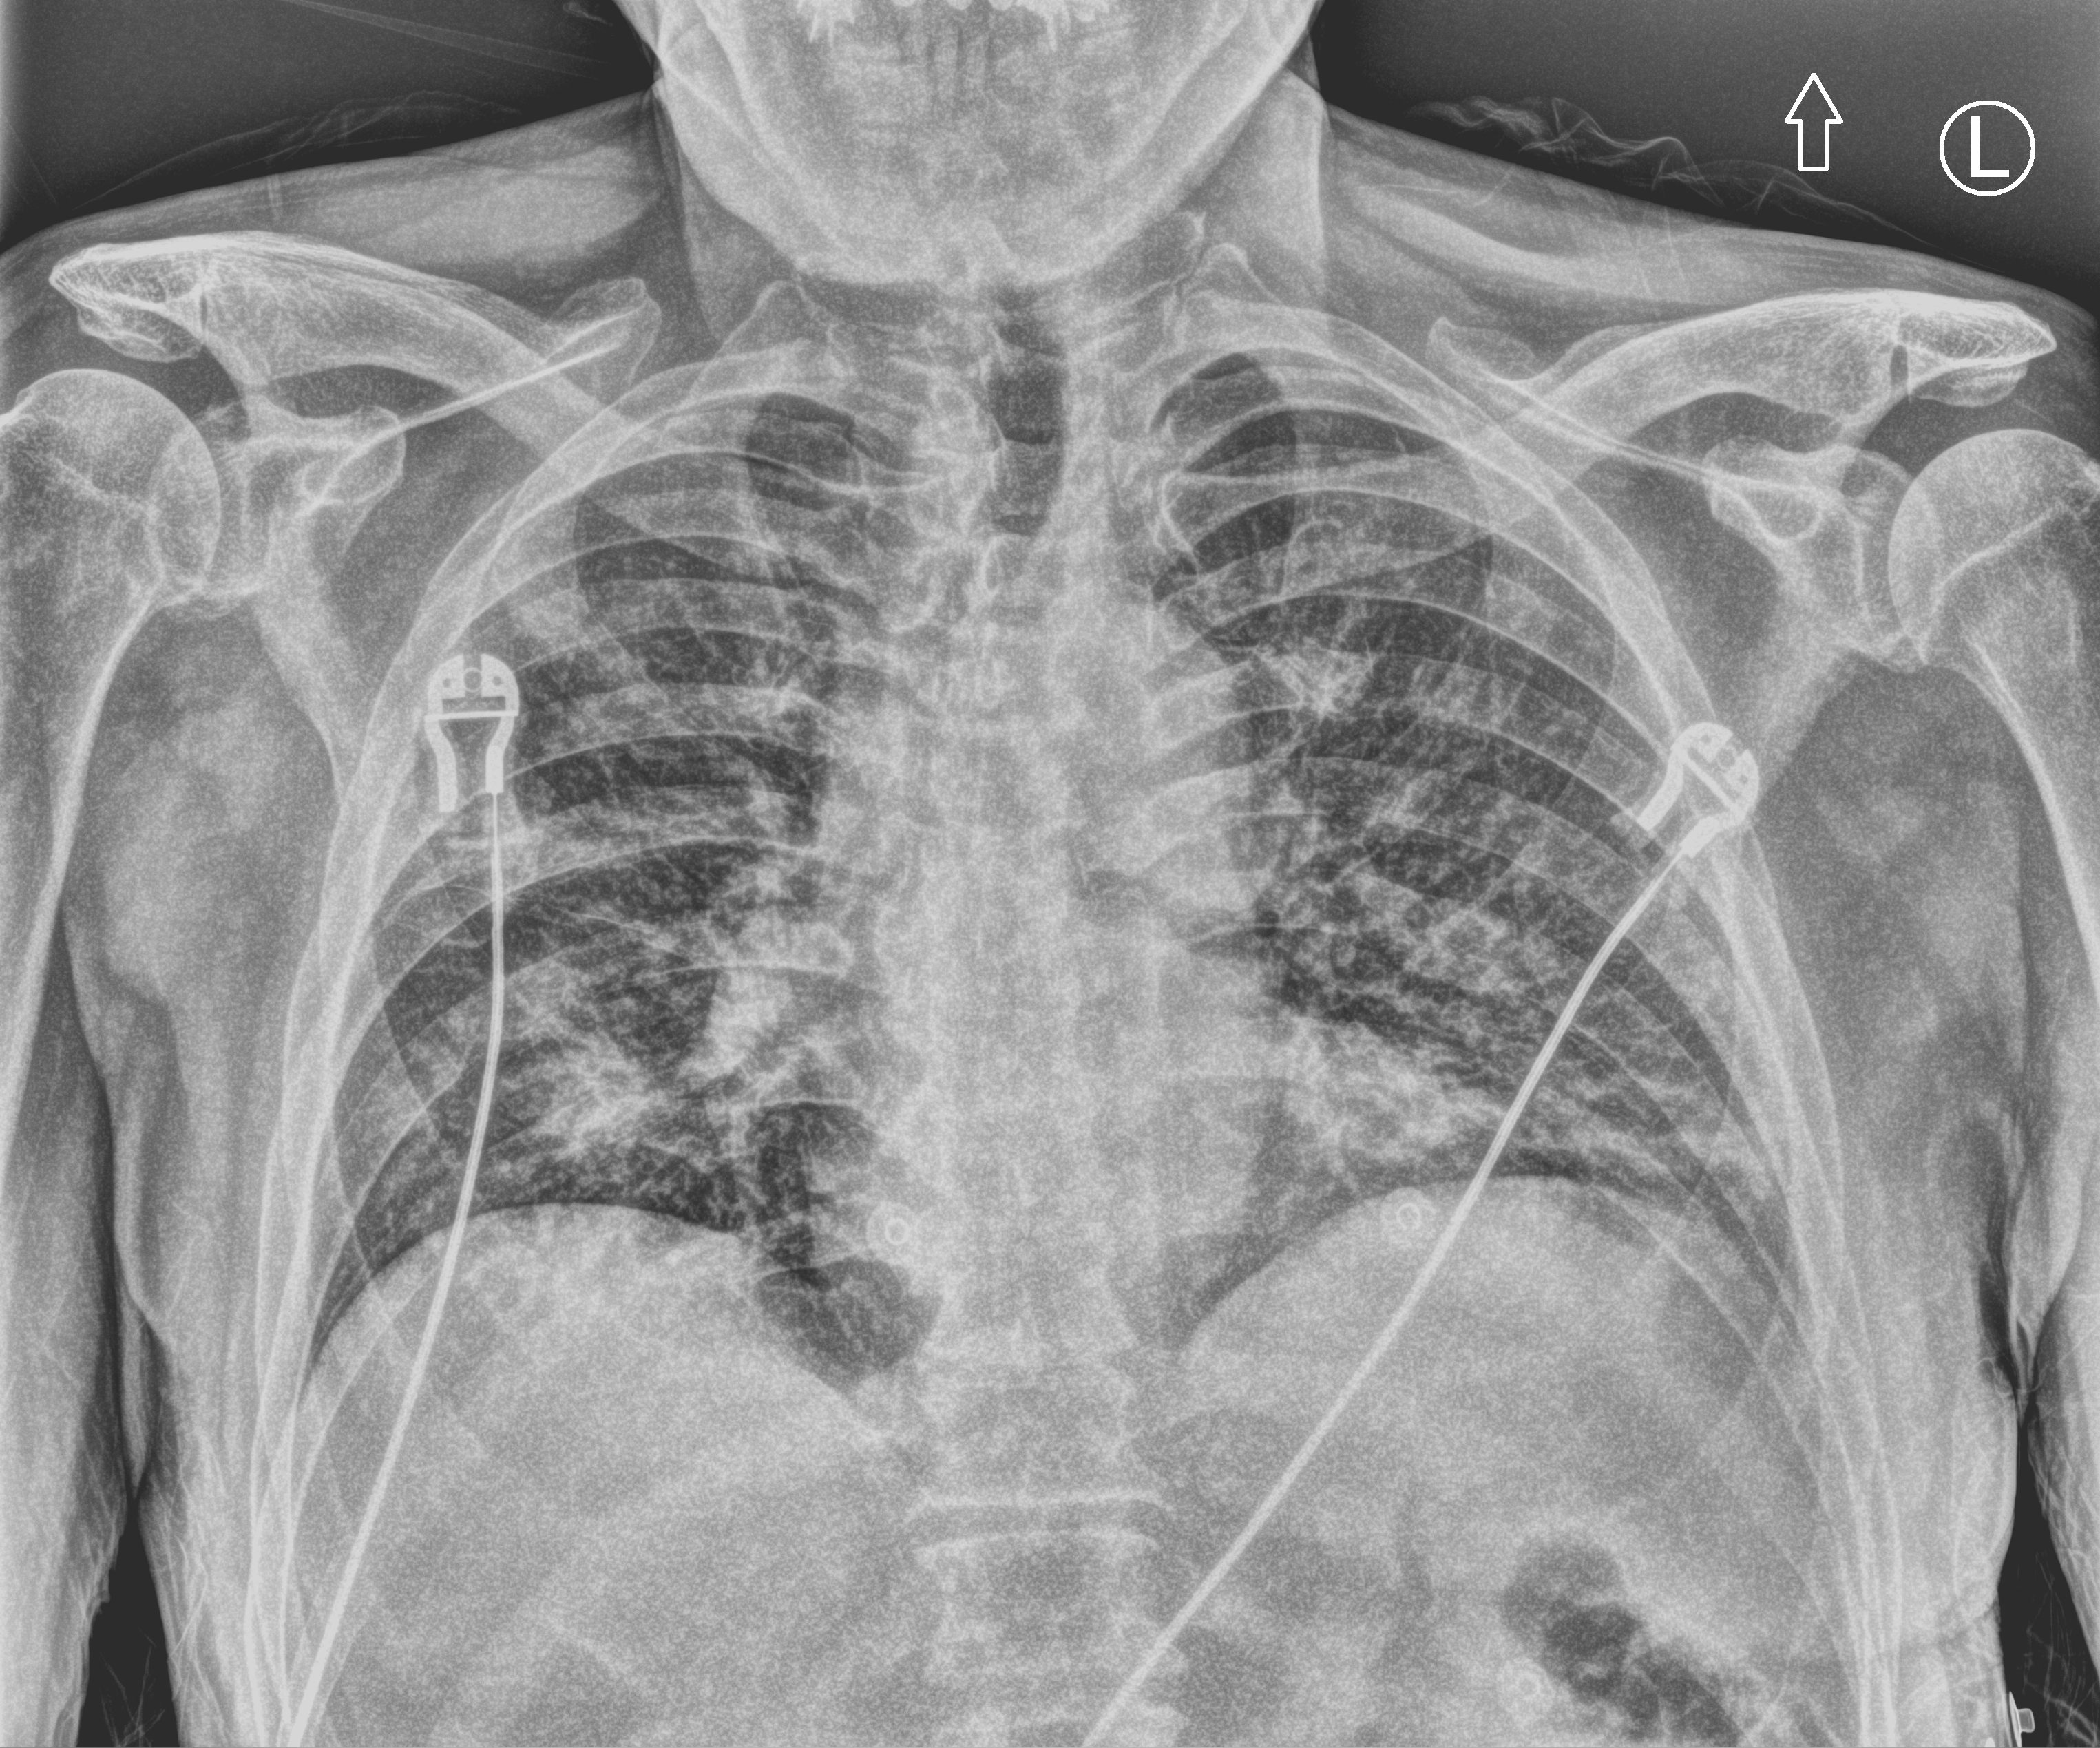
Portable chest radiograph, anteroposterior (AP) projection. Patient hospitalised with COVID-19; male, aged 60–74 years.
Hospital-stay facts (about this admission, not read from this image; timing relative to this image not recorded): COPD (admission record): no; length of hospital stay: 1 day.